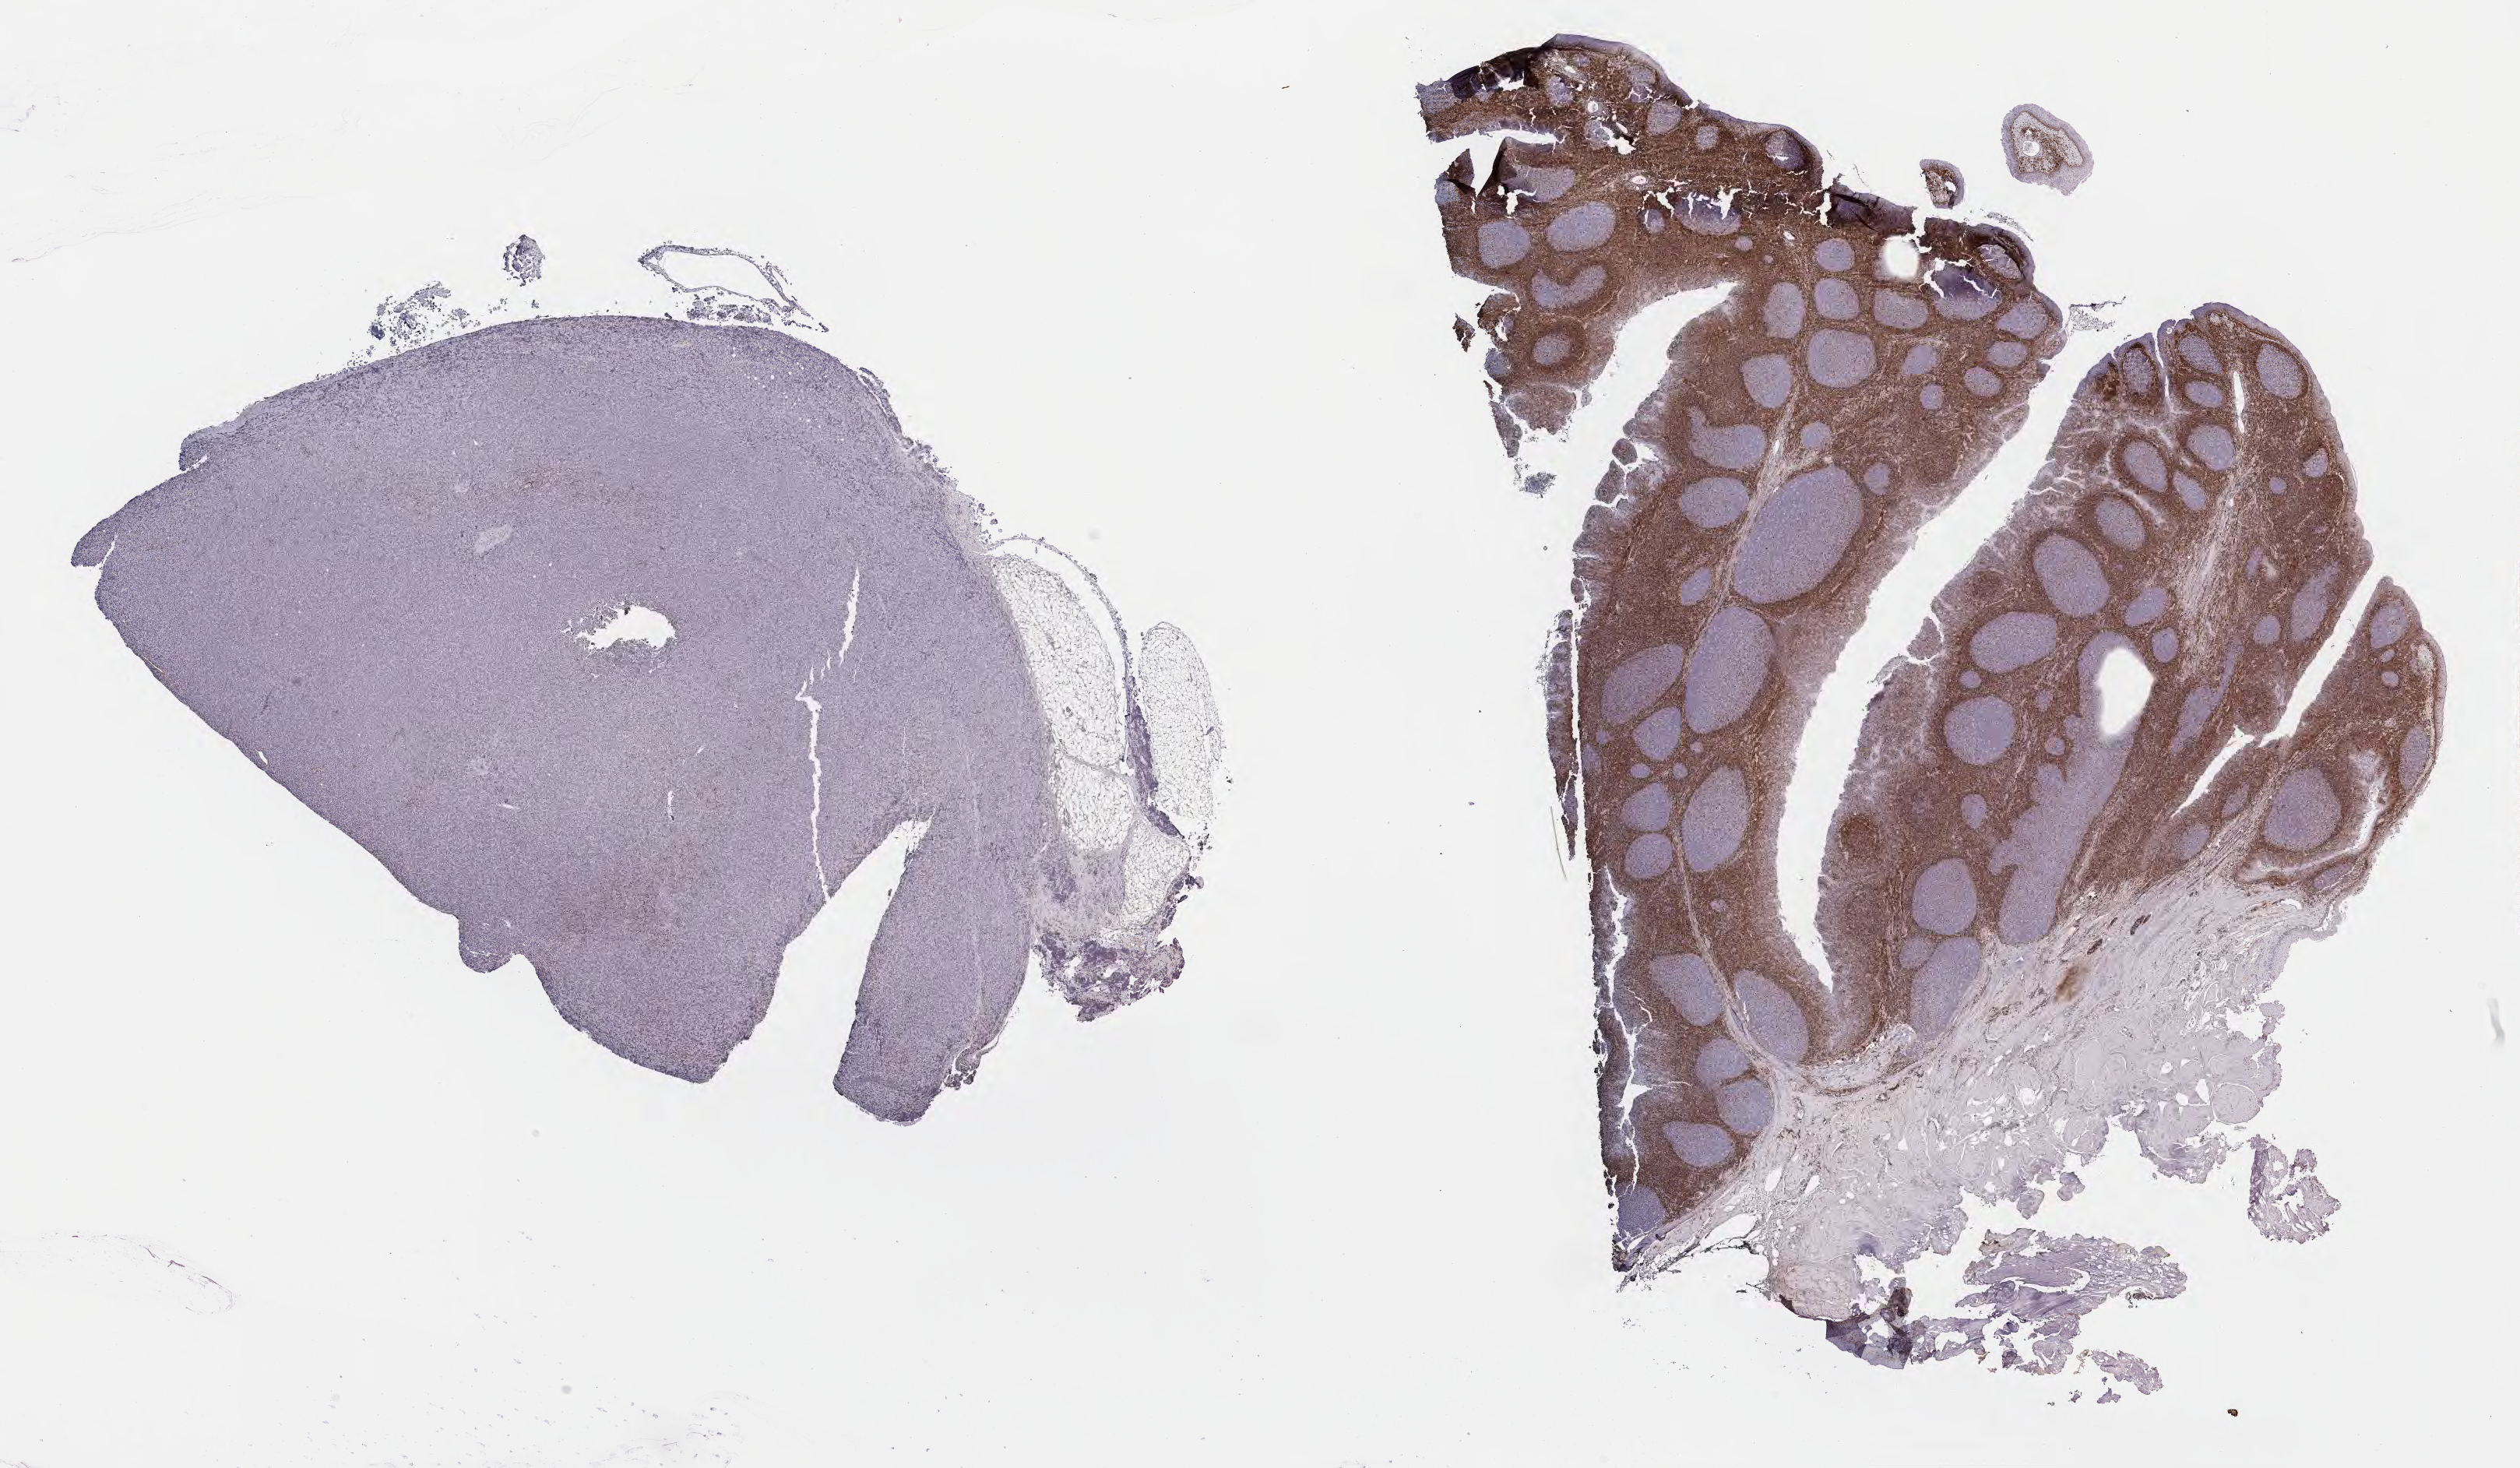
IHC for BCL2, whole-slide image — a low-resolution overview of the entire scanned area, about 26.2 x 15.2 mm; specimen: tumor tissue; site: lymph node. Male patient, 26 years old.
Diagnosis: Diffuse large B-cell lymphoma, NOS.